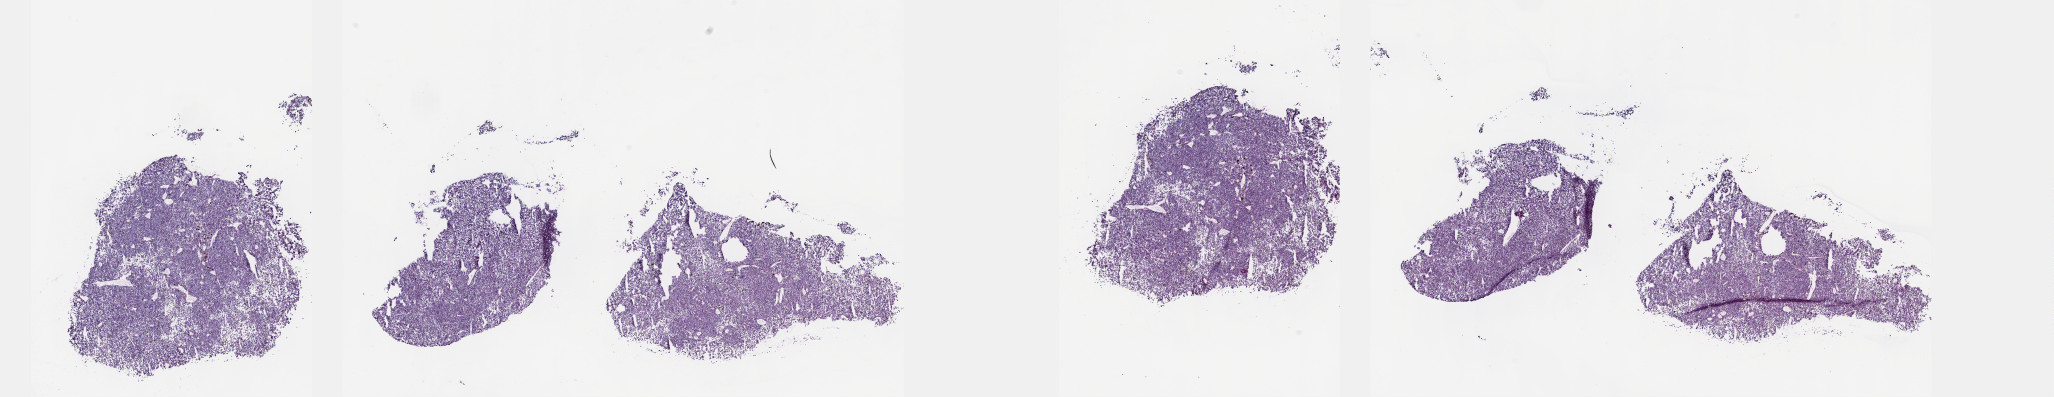
Digitized Hematoxylin and eosin (H&E) stained tissue section (whole slide) — low-resolution overview of the scanned area, about 33.2 x 6.4 mm; frozen section from the top of the tissue portion; primary tumour sample from the uvea. Male, age 78 years at initial diagnosis. Slide review estimates, as recorded: tumour cells 100%, tumour nuclei 80%, normal cells 0%, stromal cells 0%, necrosis 0%. Infiltration values recorded for this section: lymphocyte infiltration 2%, monocyte infiltration 0%, neutrophil infiltration 0%.
TNM: T4c N0 M0. AJCC pathologic stage: IIIB (7th edition). Pathologic diagnosis: Epithelioid cell melanoma (choroid).